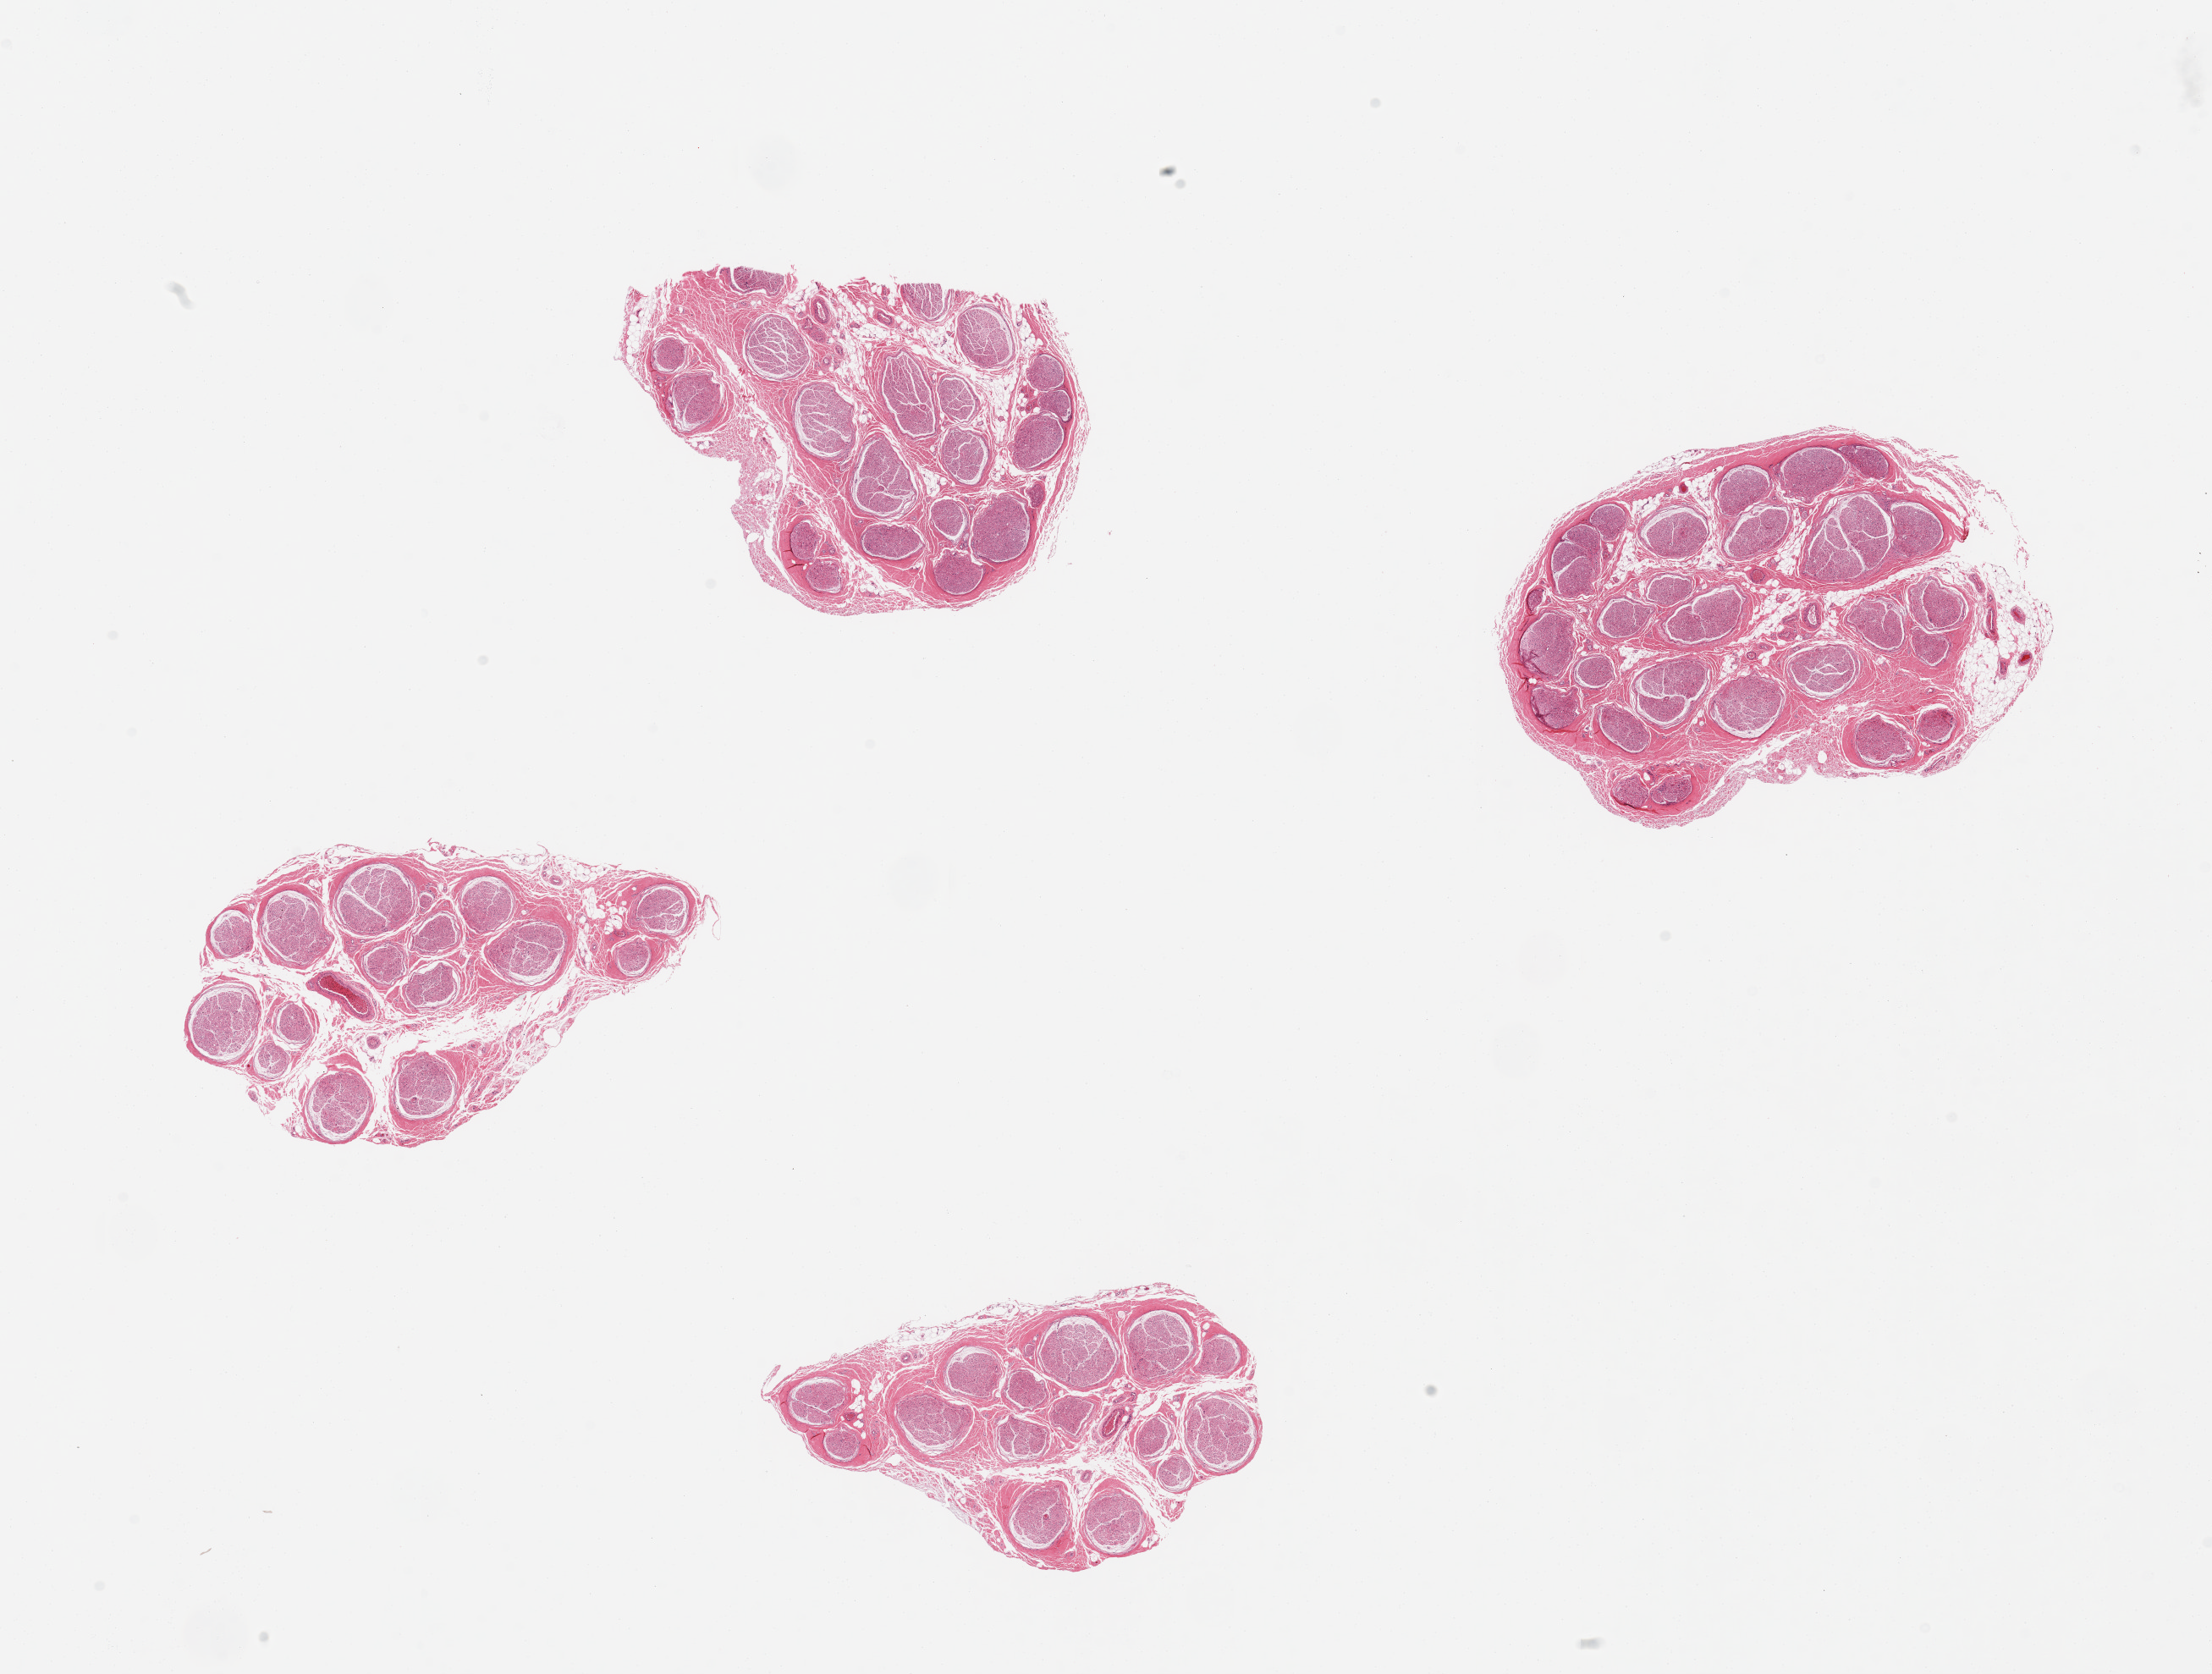
Hematoxylin and eosin (H&E) whole-slide image — low-resolution overview of the scanned area, about 20.7 x 15.6 mm (acquisition: 20x scan); PAXgene-fixed paraffin-embedded (PFPE) section; sampled site (target tissue): tibial nerve; tissue donor sample. Donor: male.
- review note (as recorded): 4 pieces, clean specimens